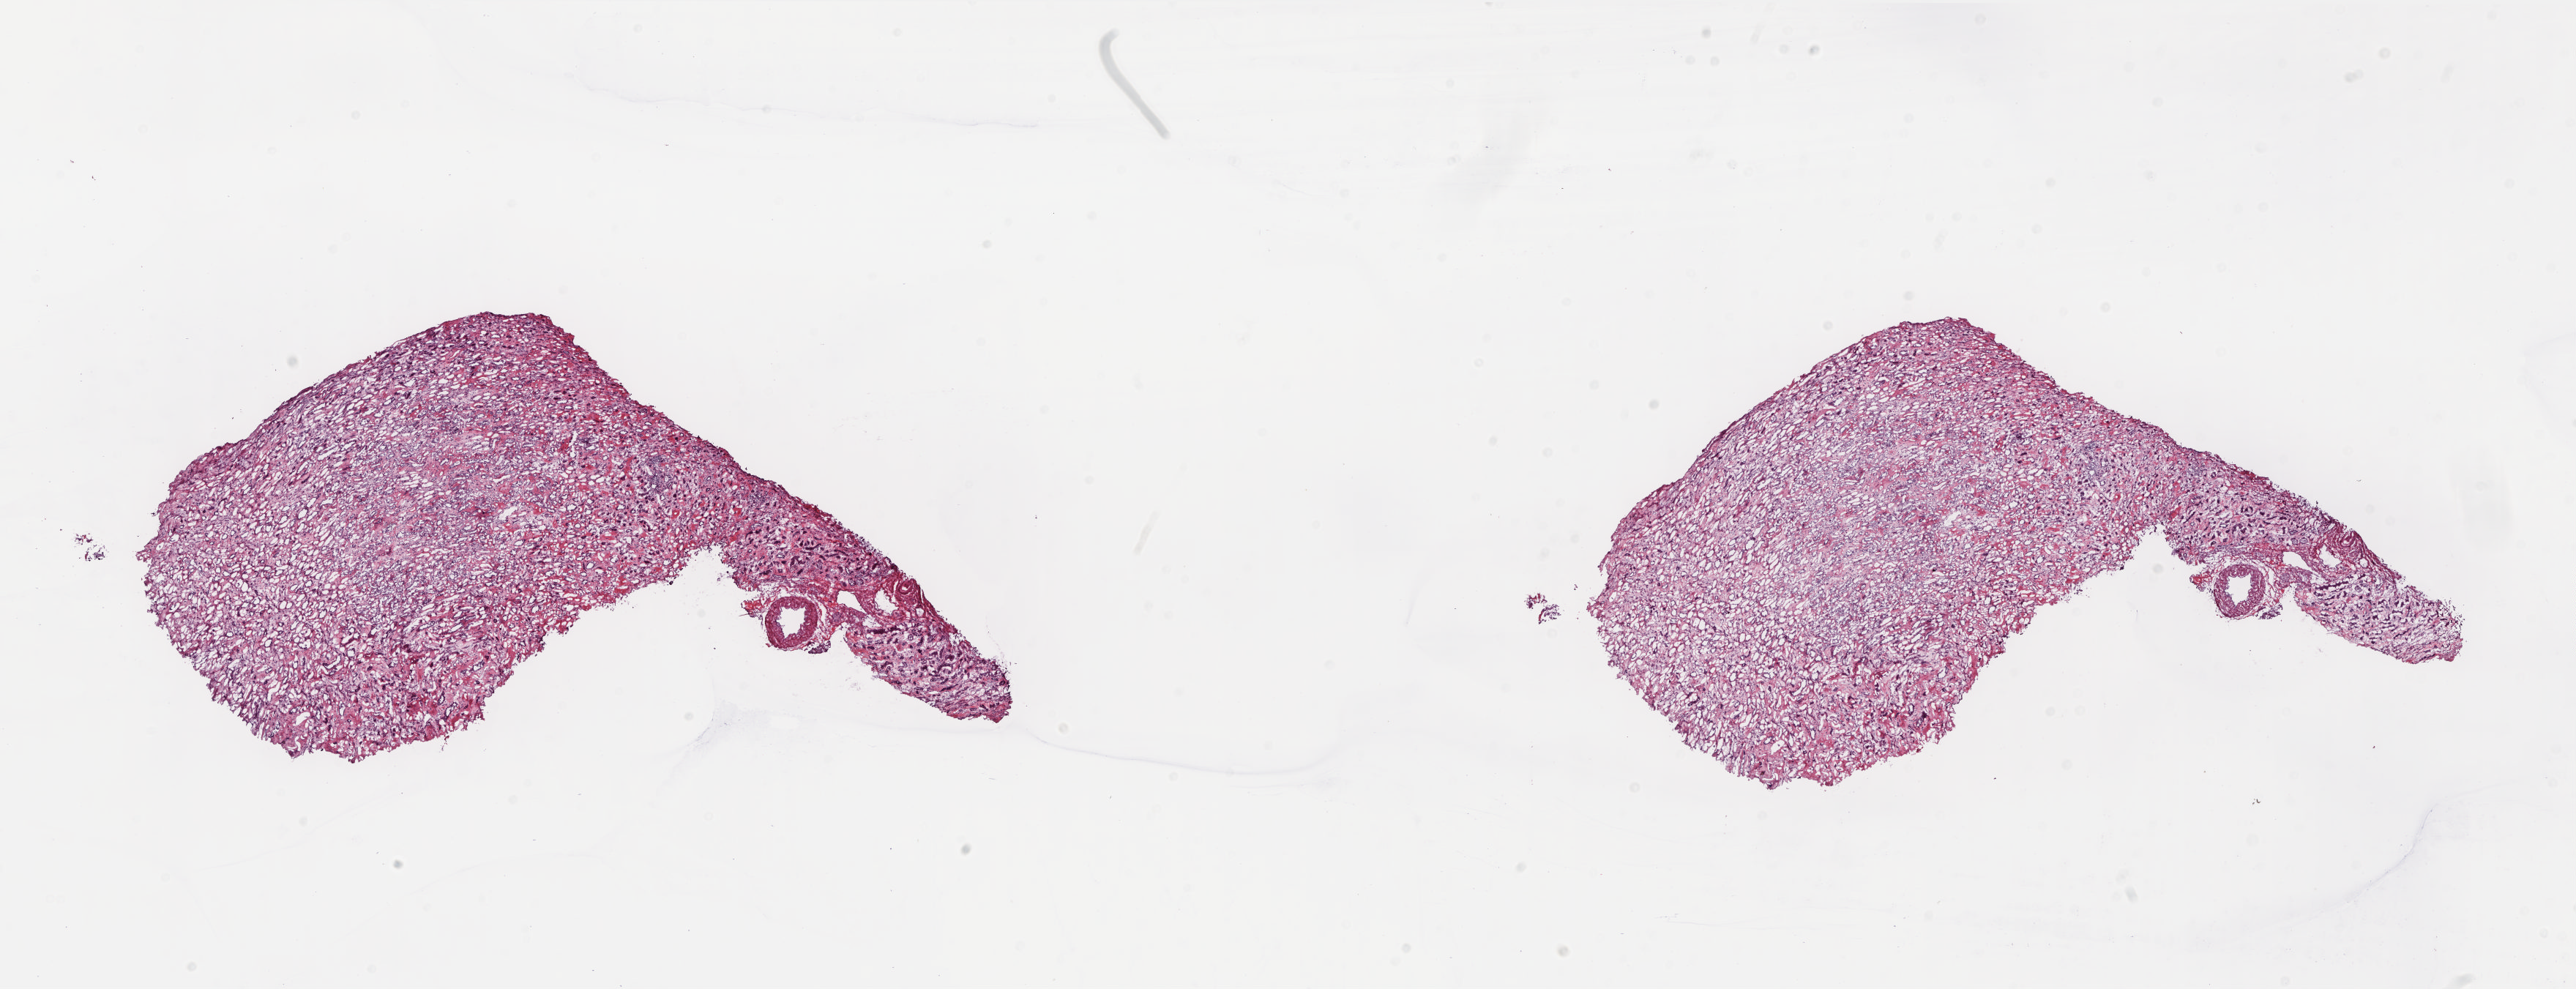
Digitized H&E tissue section (whole slide), low-resolution overview of the scanned area, about 28.4 x 10.9 mm, frozen section from the top of the tissue portion, sample: solid tissue normal (non-tumour tissue), kidney. Male patient; age at initial diagnosis 79 years. Pathologist review of this section (percent, as recorded): tumour cells 0%, tumour nuclei 0%, normal cells 100%, stromal cells 0%, necrosis 0%. Inflammatory infiltration, as recorded: lymphocyte infiltration 0%, monocyte infiltration 0%, neutrophil infiltration 0%.
This section: solid tissue normal sample (biorepository sample class). Patient diagnosis: Papillary adenocarcinoma, NOS.